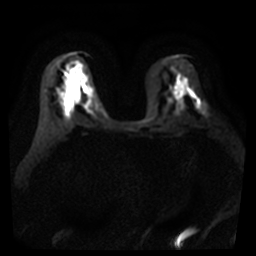
Breast MRI, one axial slice; position 21 of 40 along the scan axis; diffusion-weighted series; image 2 of 4 stored at this slice position (different b-values; order by instance number); 3 T; 5 mm slice thickness; 256 × 256 image matrix, field of view 360 × 360 mm. Female patient.
Structures marked on this image (manually delineated by an expert):
- tumour on diffusion-weighted imaging: bounding box [x1, y1, x2, y2] px = [198, 103, 208, 115]